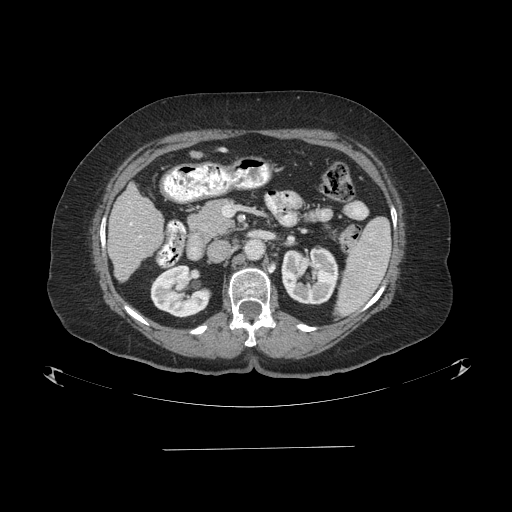
Contrast-enhanced abdominal CT (liver protocol), one axial slice; slice 35 of 103 in the series (ordered by position); 120 kVp; one of 2 acquisitions stored at this slice position; soft-tissue window (W 400 / L 40 HU); 512 × 512 image matrix. From the clinical record (not read from this slice): diagnosis: hepatocellular carcinoma (patient treated with transarterial chemoembolisation; whether this scan precedes or follows treatment is not stated here); TNM stage (as recorded): Stage-IIIA; Child-Pugh class: A; tumour differentiation: poorly differentiated.
Annotated regions visible in this slice (semi-automatically segmented with operator editing):
- liver parenchyma outside the tumour (the mass and vessels are separate outlines, so this box may not span the whole liver): box from (x=108, y=184) to (x=164, y=280) px
- liver vessels: (x=130, y=222)–(x=141, y=238)